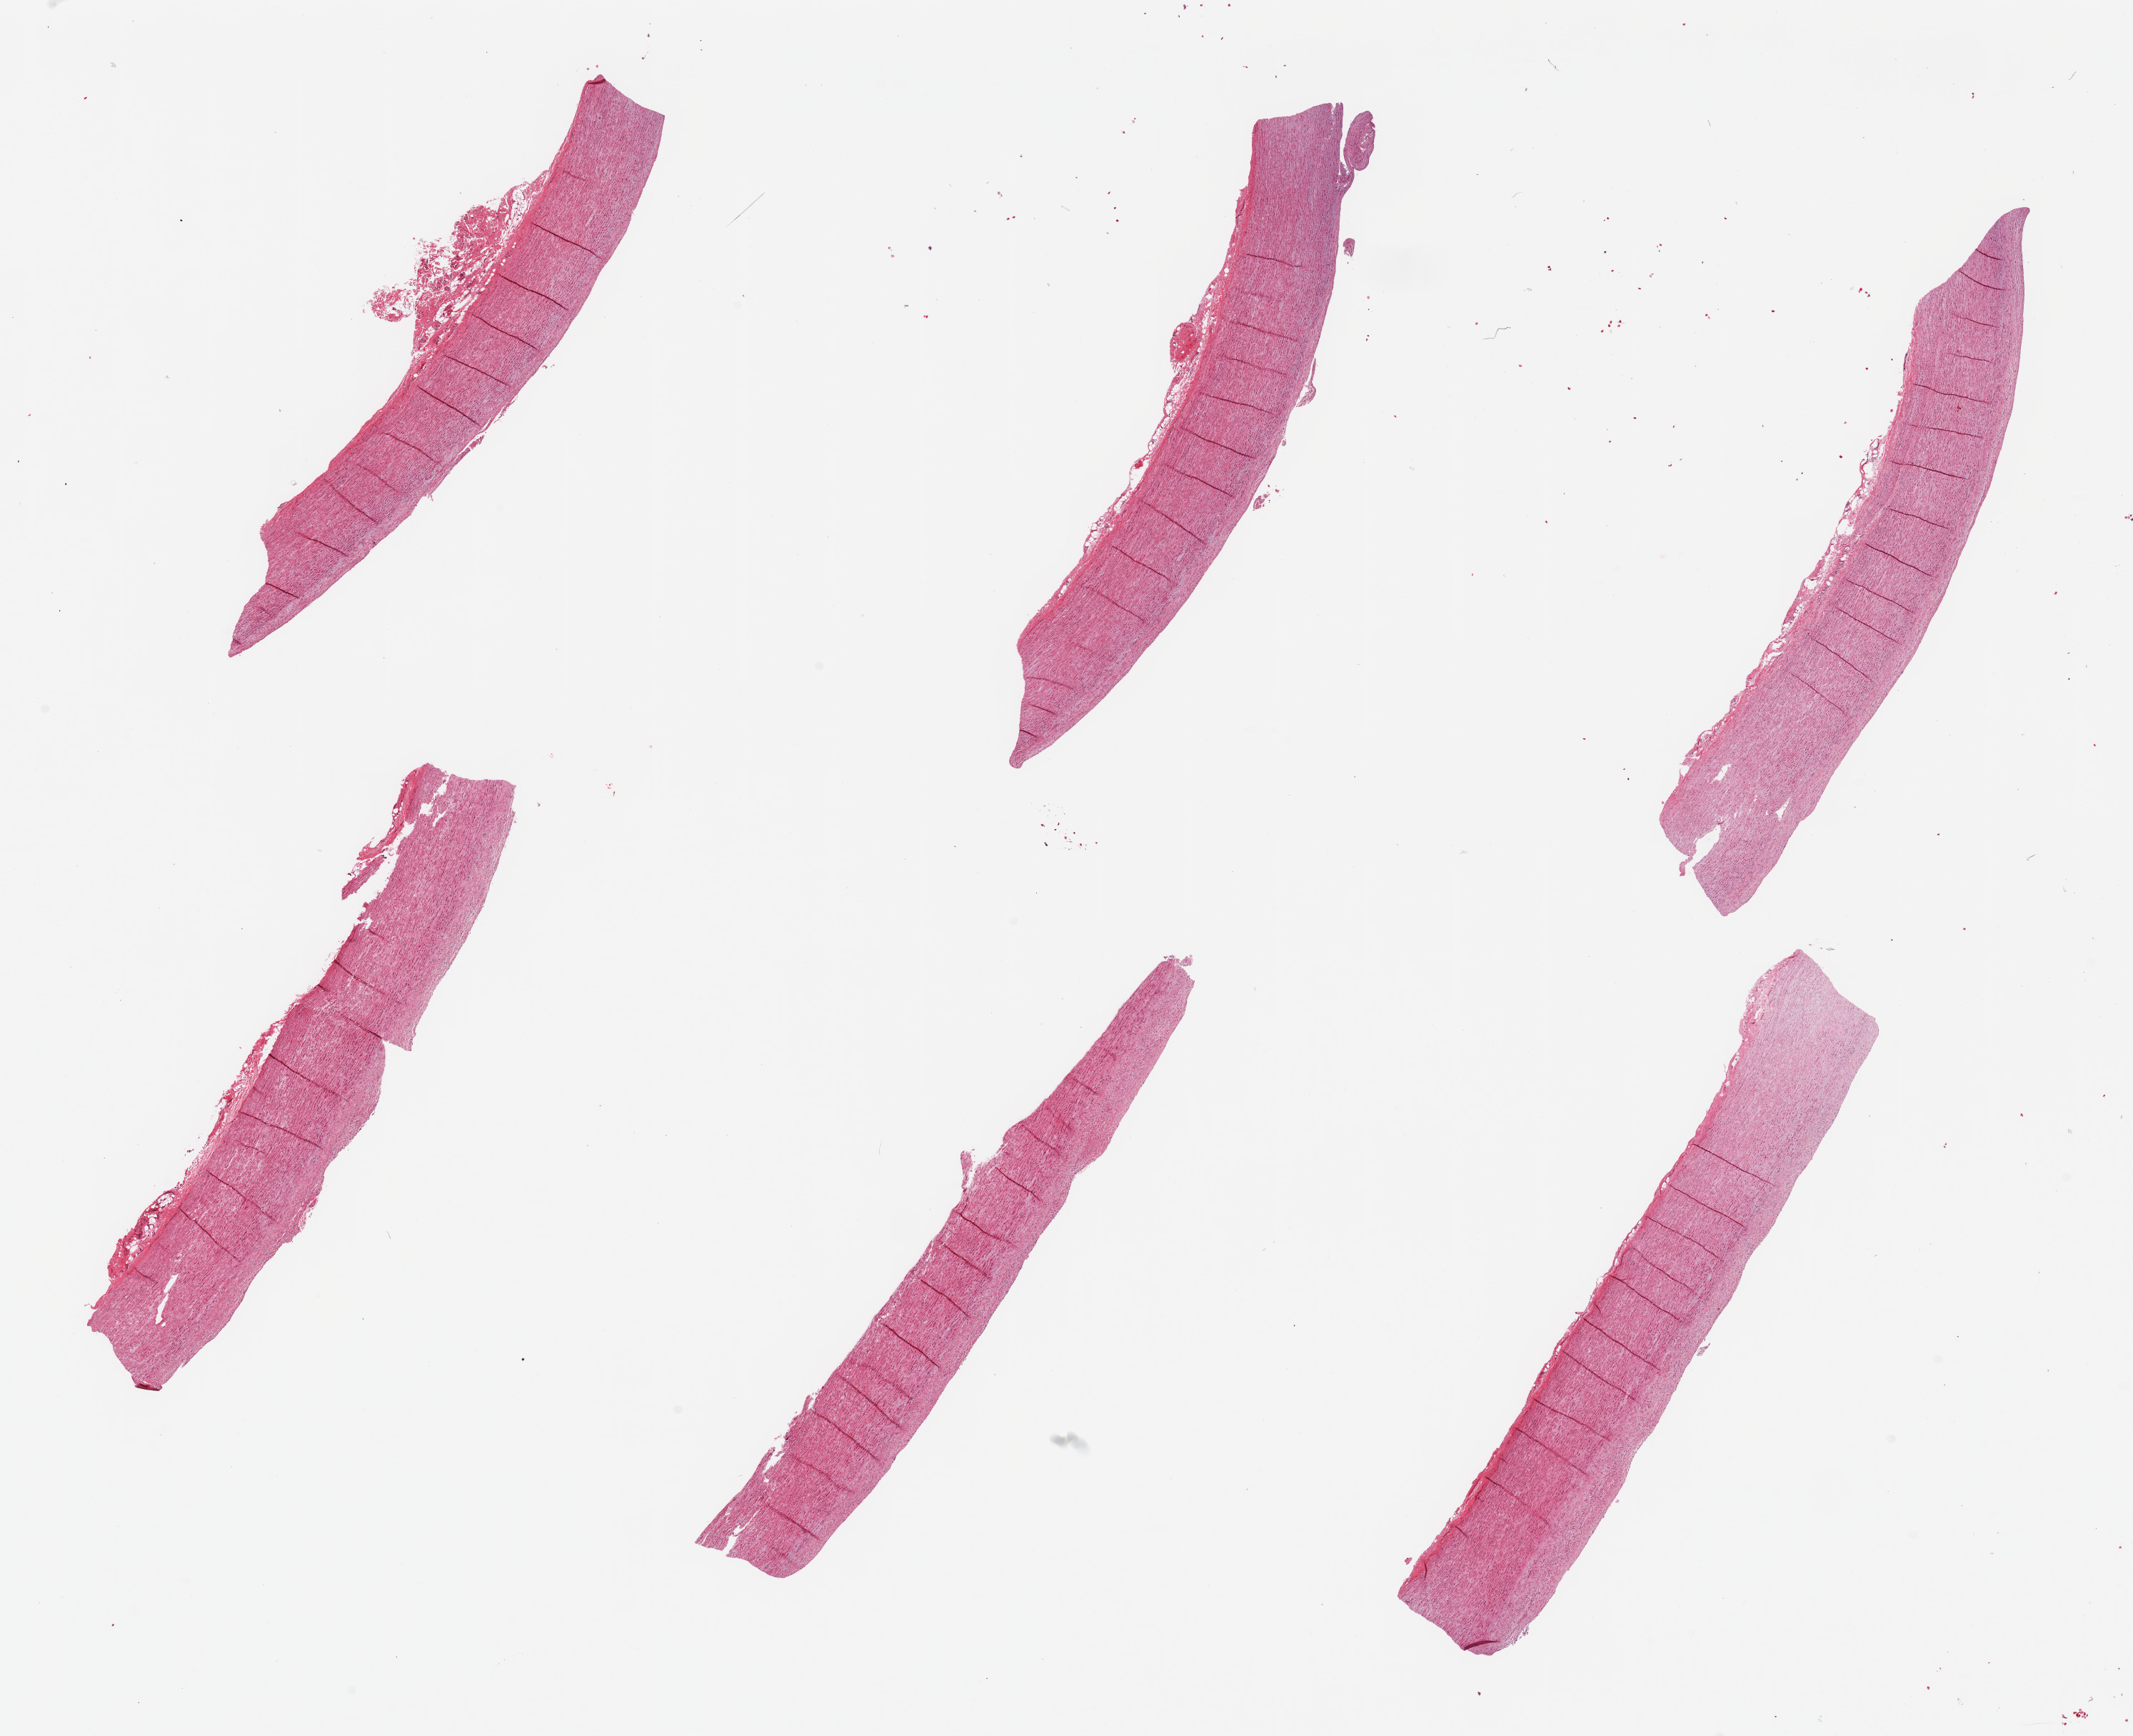
Whole-slide image, H&E stain — shown as a low-resolution overview of the whole scanned area (about 23.6 x 19.2 mm, slide scanned at 20x); PAXgene-fixed, paraffin-embedded tissue; target tissue: aorta; donor tissue sample. Donor: male.
Reviewer comment on this tissue sample: 6 pieces, minimal atherosis.